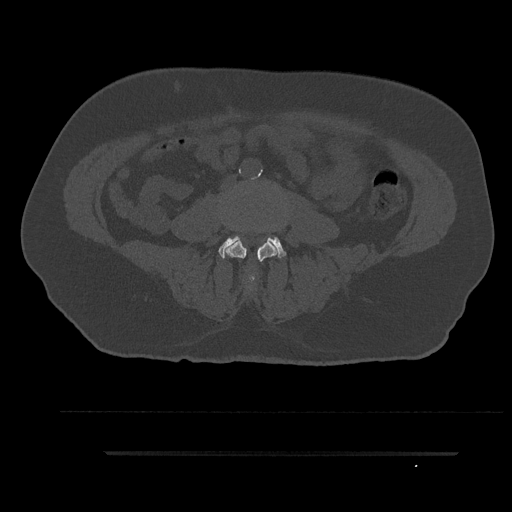
CT including the spine, one axial slice. Slice 10 of 797 in the series (ordered by position). Reconstruction kernel Br40s/3. Bone window (W 1800 / L 400 HU). 0.5 mm slice thickness. 512 × 512 image matrix, field of view 432 × 432 mm. Male patient, age 63 years. Case-level facts recorded for this patient, not image findings: primary cancer: renal; vertebrae with lytic lesions (as recorded): T8.
Outlined on this slice (semi-automatic segmentation, software-assisted and operator-edited):
- L3 vertebra: bounding box <225,223,276,285> (left, top, right, bottom; pixels)
- L4 vertebra: <218,236,286,259>